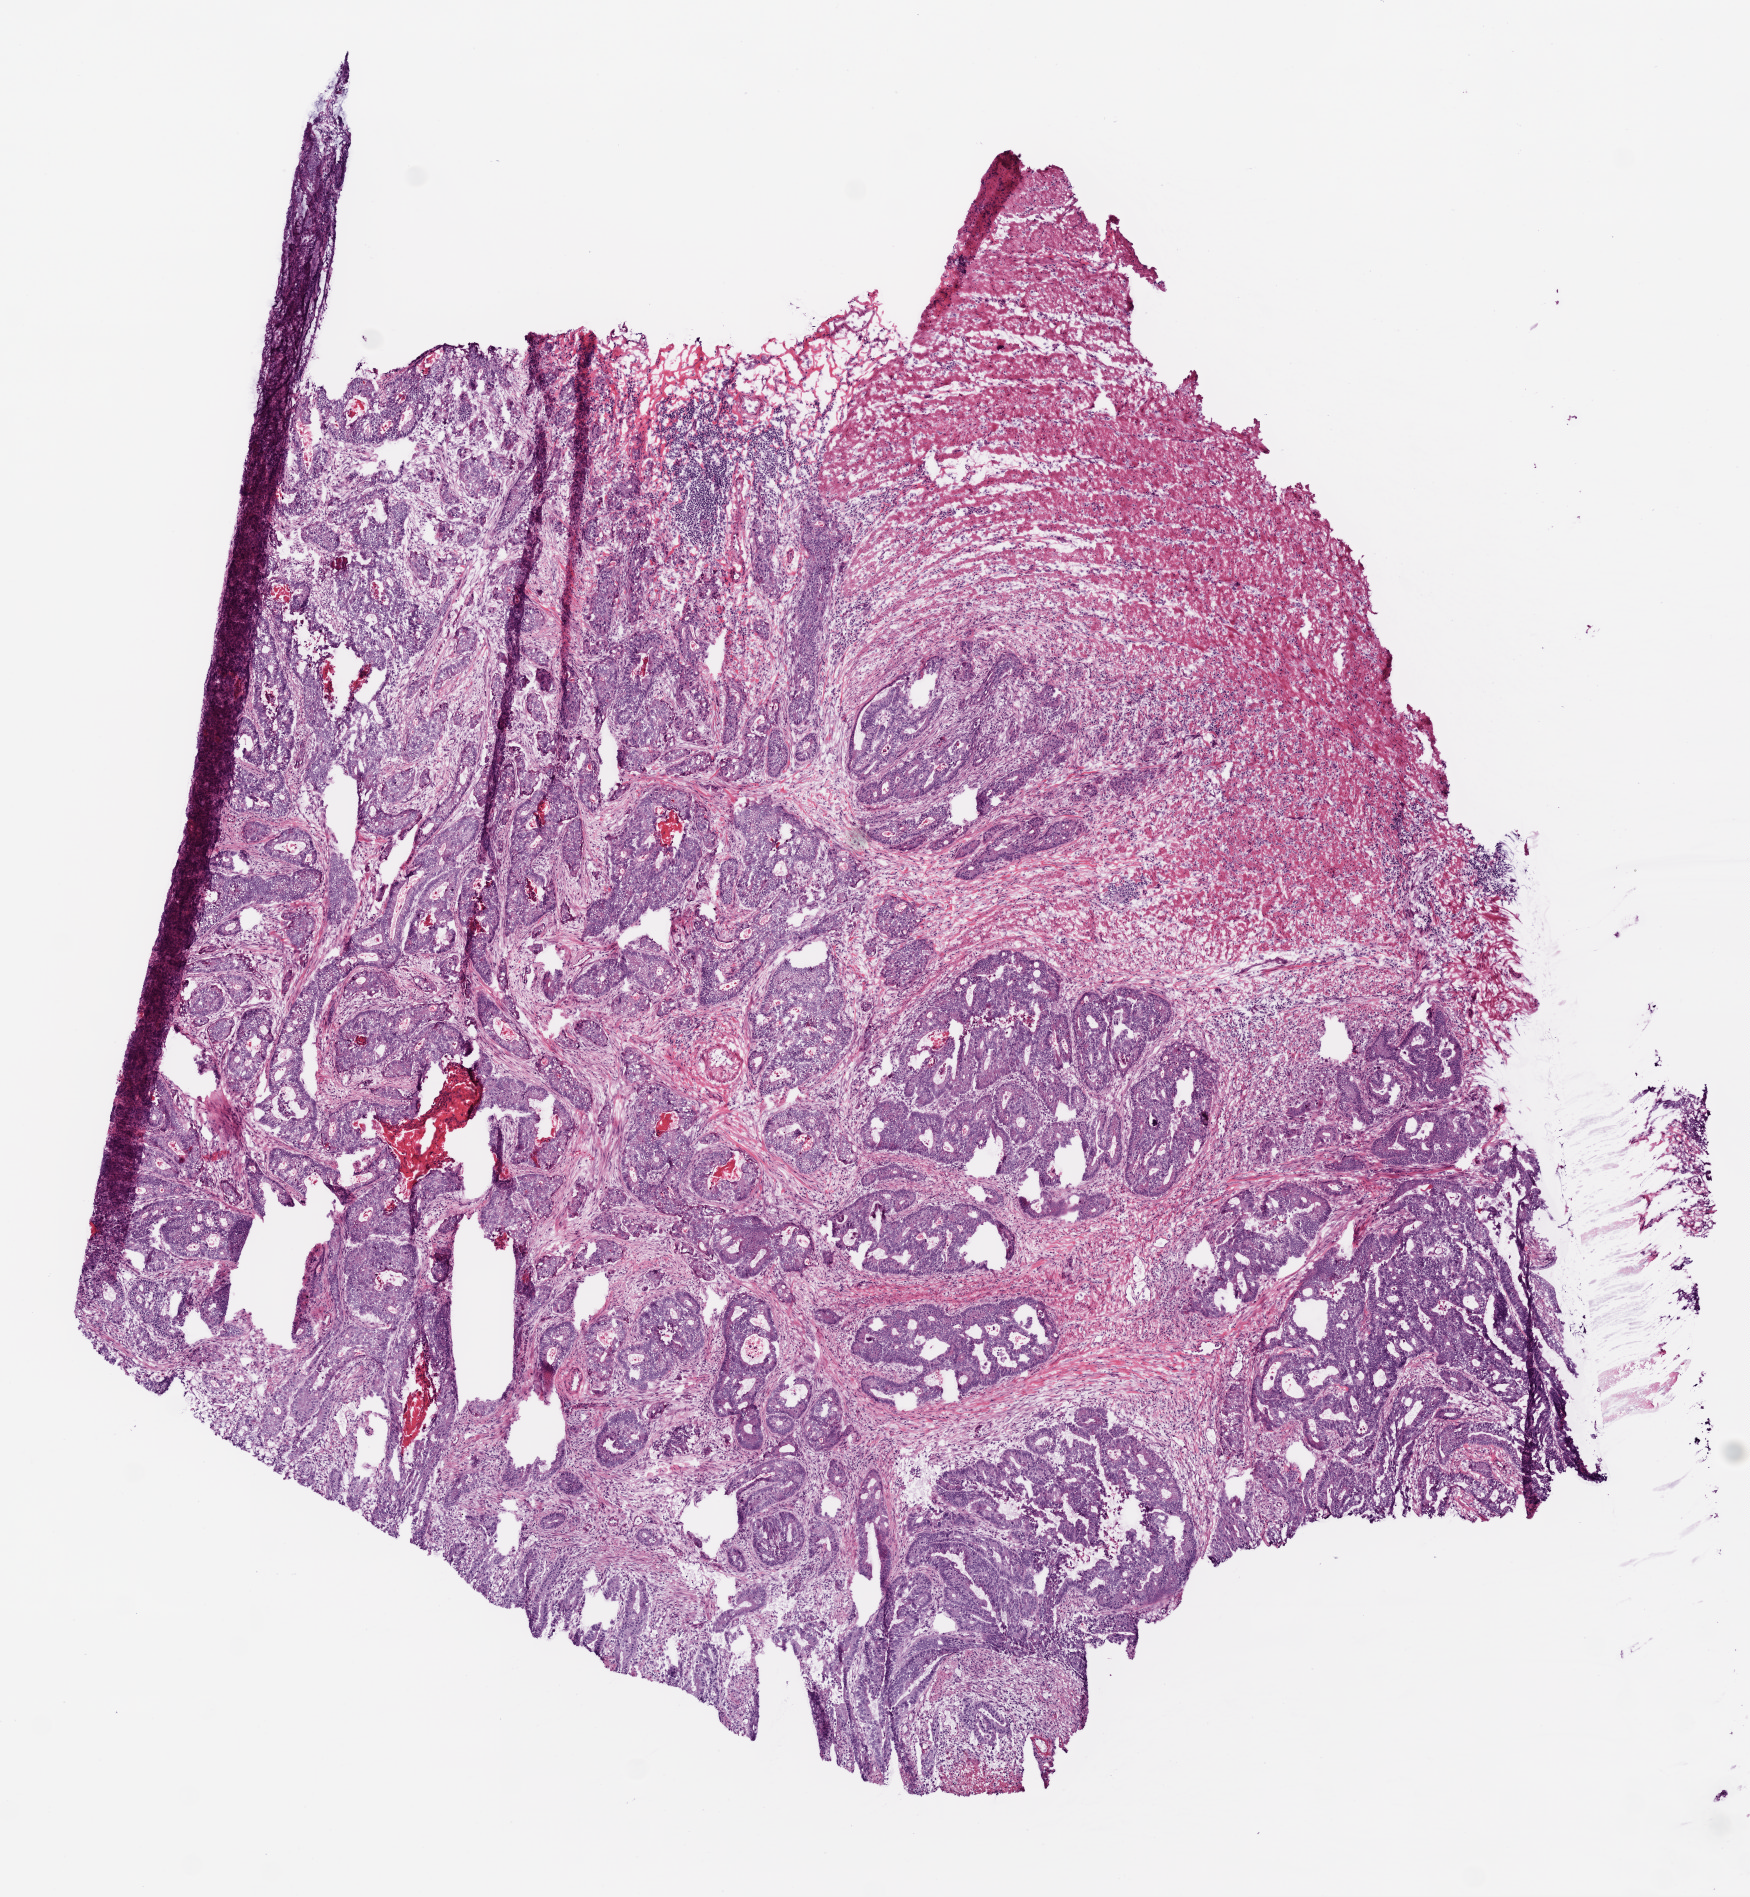
Whole-slide histology image, H&E, low-resolution overview of the scanned area, about 7.0 x 7.6 mm. Frozen section from the top of the tissue portion. Sample: primary tumour, rectum. Female, age 59 years at initial diagnosis. Slide review estimates, as recorded: tumour cells 72%, tumour nuclei 80%, normal cells 8%, stromal cells 15%, necrosis 5%.
Histologic diagnosis: Adenocarcinoma, NOS. AJCC pathologic stage: II (5th edition).